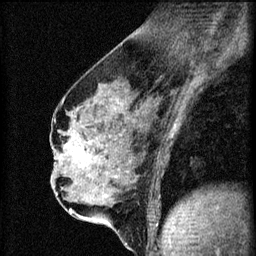
Breast MRI (dynamic contrast-enhanced), one sagittal slice; slice 34 of 60 in the series (ordered by position); 3 images stored at this slice position (order not interpretable as contrast timing); 1.5 T; TE 4.2 ms, TR 8.2 ms; 2 mm slice thickness; 256 × 256 image matrix, field of view 180 × 180 mm. Female patient, age 56 years.
Outlined on this slice (semi-automatically segmented with operator editing):
- analysis volume of interest (the breast-tissue region the enhancement analysis was run in; not a lesion): box from (x=62, y=136) to (x=111, y=179) px
- tumour enhancement mask (voxels above the 70 % enhancement threshold inside the analysis volume of interest): (x=62, y=138)–(x=90, y=161)